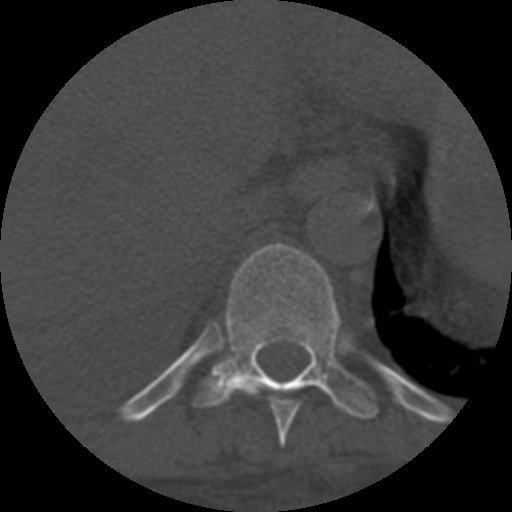
CT including the spine, one axial slice; position 363 of 708 along the scan axis; reconstruction kernel STANDARD; 120 kVp; one of 3 acquisitions stored at this slice position; bone window (W 1800 / L 400 HU); 512 × 512 image matrix, field of view 160 × 160 mm. Patient age 55 years. Case-level facts recorded for this patient, not image findings: primary cancer: colon.
Annotated regions visible in this slice (semi-automatically segmented with operator editing):
- T10 vertebra: bounding box (x1, y1, x2, y2) in pixels: (194, 244, 377, 419)
- T9 vertebra: (236, 389, 299, 446)